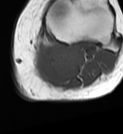
MRI of an extremity soft-tissue mass, one axial slice. Position 46 of 68 along the scan axis. MR volume resampled by the dataset authors to the PET/CT grid (not the native acquisition matrix). 123 × 134 image matrix, field of view 120 × 131 mm. Female patient. Case-level facts recorded for this patient, not image findings: histological type: extraskeletal high grade osteogenic sarcoma; grade: high; site of the primary tumour: left calf.
Structures marked on this image (expert contour drawn on MRI and transferred to this co-registered scan by the dataset authors):
- gross tumour volume (mass): bounding box <31,41,84,83> (left, top, right, bottom; pixels)